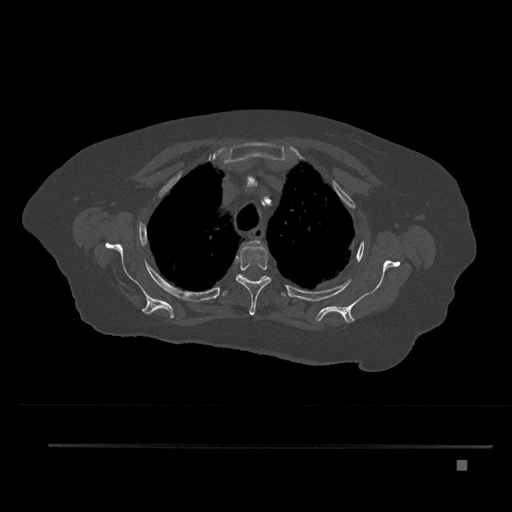
CT including the spine, one axial slice; position 633 of 797 along the scan axis; 120 kVp; bone window (W 1800 / L 400 HU); 0.5 mm slice thickness; 512 × 512 image matrix. Patient: female, 76 years. Case-level facts recorded for this patient, not image findings: primary cancer: lung.
Annotated regions visible in this slice (semi-automatically segmented with operator editing):
- T2 vertebra: bounding box [x1, y1, x2, y2] px = [242, 240, 264, 246]
- T3 vertebra: [235, 245, 272, 315]
- T4 vertebra: [223, 274, 286, 297]